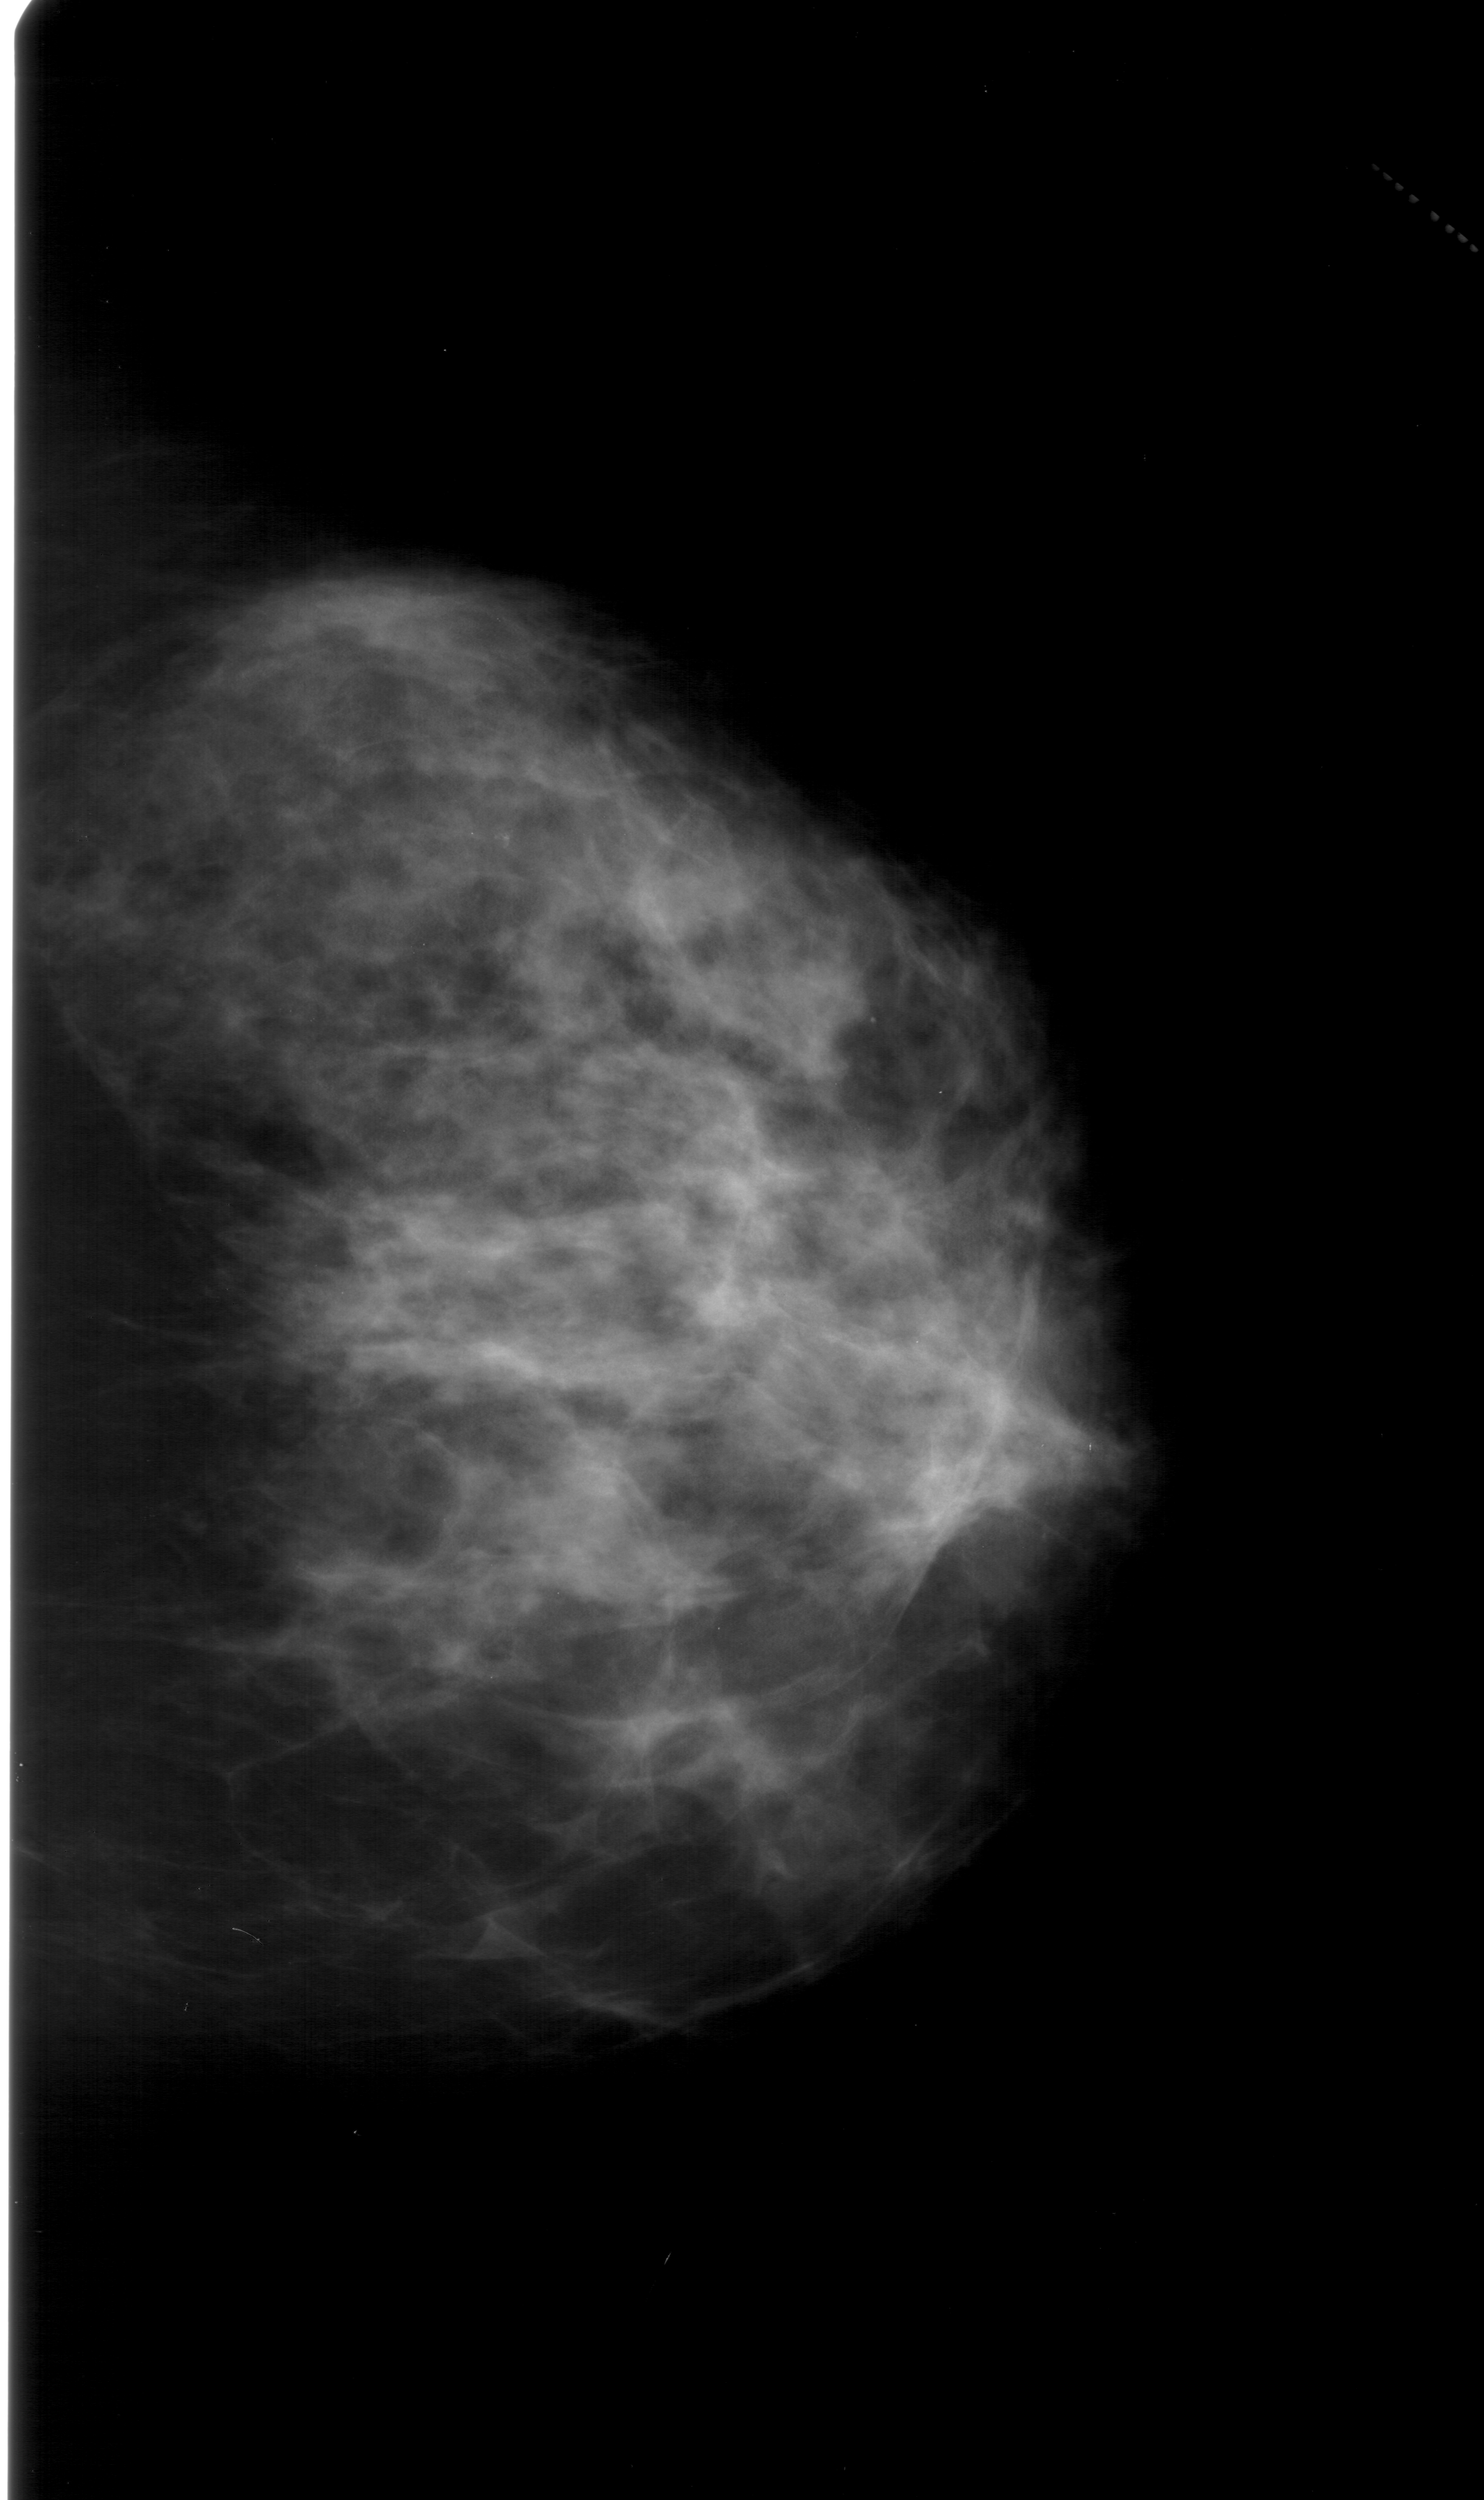
Scanned film-screen mammogram. Right breast. Craniocaudal (CC) view. BI-RADS breast density category 3 (scale 1–4). 1484 × 2500 image matrix.
Marked abnormalities (boxes around the expert regions of interest):
- calcifications, morphology pleomorphic, distribution clustered; BI-RADS assessment category 4; subtlety rating 2 on a 1 (subtle) to 5 (obvious) scale; pathology result (as recorded, not read from the image): benign: bounding box <477,818,534,865> (left, top, right, bottom; pixels)